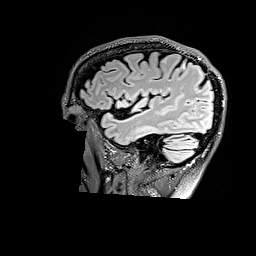
Brain MRI from a brain-tumour surgery series, one sagittal slice. Slice 131 of 176 in the series (ordered by position). T2 FLAIR. 1 mm slice thickness. 256 × 256 image matrix, field of view 256 × 256 mm. From the clinical record (not read from this slice): histopathology: Astrocytoma; WHO grade: 3; IDH mutation: yes.
Structures marked on this image (manually delineated by an expert):
- tumour: box from (x=180, y=62) to (x=185, y=69) px